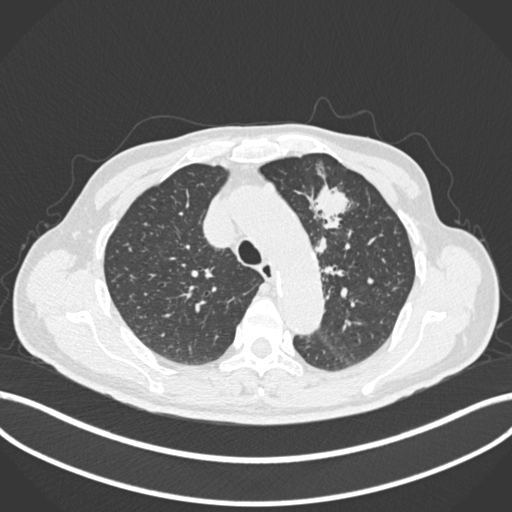
Chest CT, one axial slice. Slice 185 of 261 in the series (ordered by position). Reconstruction kernel B30f. Lung window (W 1500 / L -600 HU). 512 × 512 image matrix. Male patient, age 74 years. Case-level facts recorded for this patient, not image findings: clinical TNM (as recorded): T2b N0 M1c.
Outlined on this slice (bounding box drawn by a radiologist):
- lung tumour (recorded histology: adenocarcinoma): box from (x=301, y=171) to (x=356, y=239) px